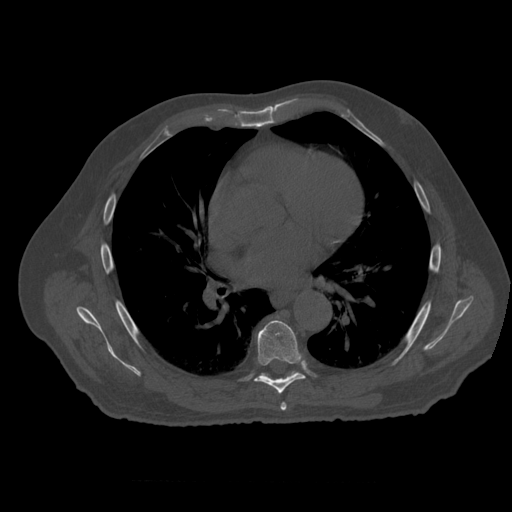
CT including the spine, one axial slice; position 359 of 399 along the scan axis; reconstruction kernel STANDARD; 120 kVp; bone window (W 1800 / L 400 HU); 1.25 mm slice thickness; 512 × 512 image matrix, field of view 407 × 407 mm. Patient age 73 years. From the clinical record (not read from this slice): primary cancer: prostate; vertebrae with lytic lesions (as recorded): L2.
Structures marked on this image (semi-automatically segmented with operator editing):
- T6 vertebra: bounding box <281,403,287,413> (left, top, right, bottom; pixels)
- T7 vertebra: <255,321,305,394>
- T8 vertebra: <263,372,295,375>